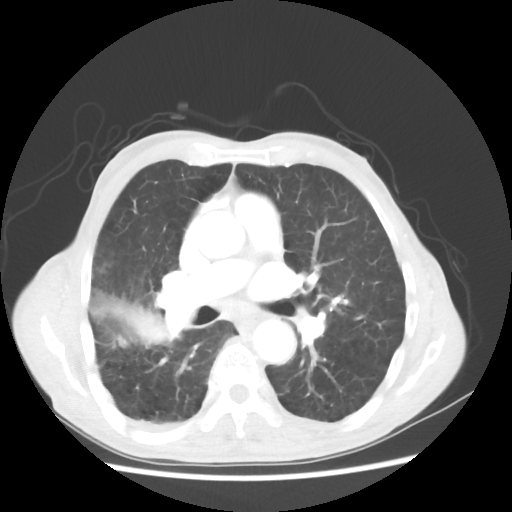
Chest CT, one axial slice; slice 29 of 58 in the series (ordered by position); reconstruction kernel STANDARD; 100 kVp; lung window (W 1500 / L -600 HU); 5 mm slice thickness; 512 × 512 image matrix, field of view 351 × 351 mm. Male patient, age 75 years. Case-level facts recorded for this patient, not image findings: clinical TNM (as recorded): T4 N1 M1.
Structures marked on this image (bounding box drawn by a radiologist):
- lung tumour (recorded histology: adenocarcinoma): box from (x=87, y=286) to (x=179, y=350) px